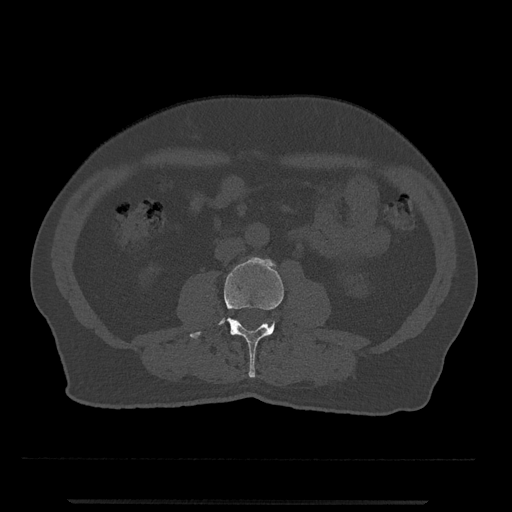
CT including the spine, one axial slice. Slice 195 of 797 in the series (ordered by position). 120 kVp. Bone window (W 1800 / L 400 HU). 0.5 mm slice thickness. 512 × 512 image matrix, field of view 419 × 419 mm. Male patient, age 63 years. From the clinical record (not read from this slice): primary cancer: prostate.
Outlined on this slice (semi-automatically segmented with operator editing):
- L3 vertebra: bounding box (x1, y1, x2, y2) in pixels: (189, 257, 284, 378)